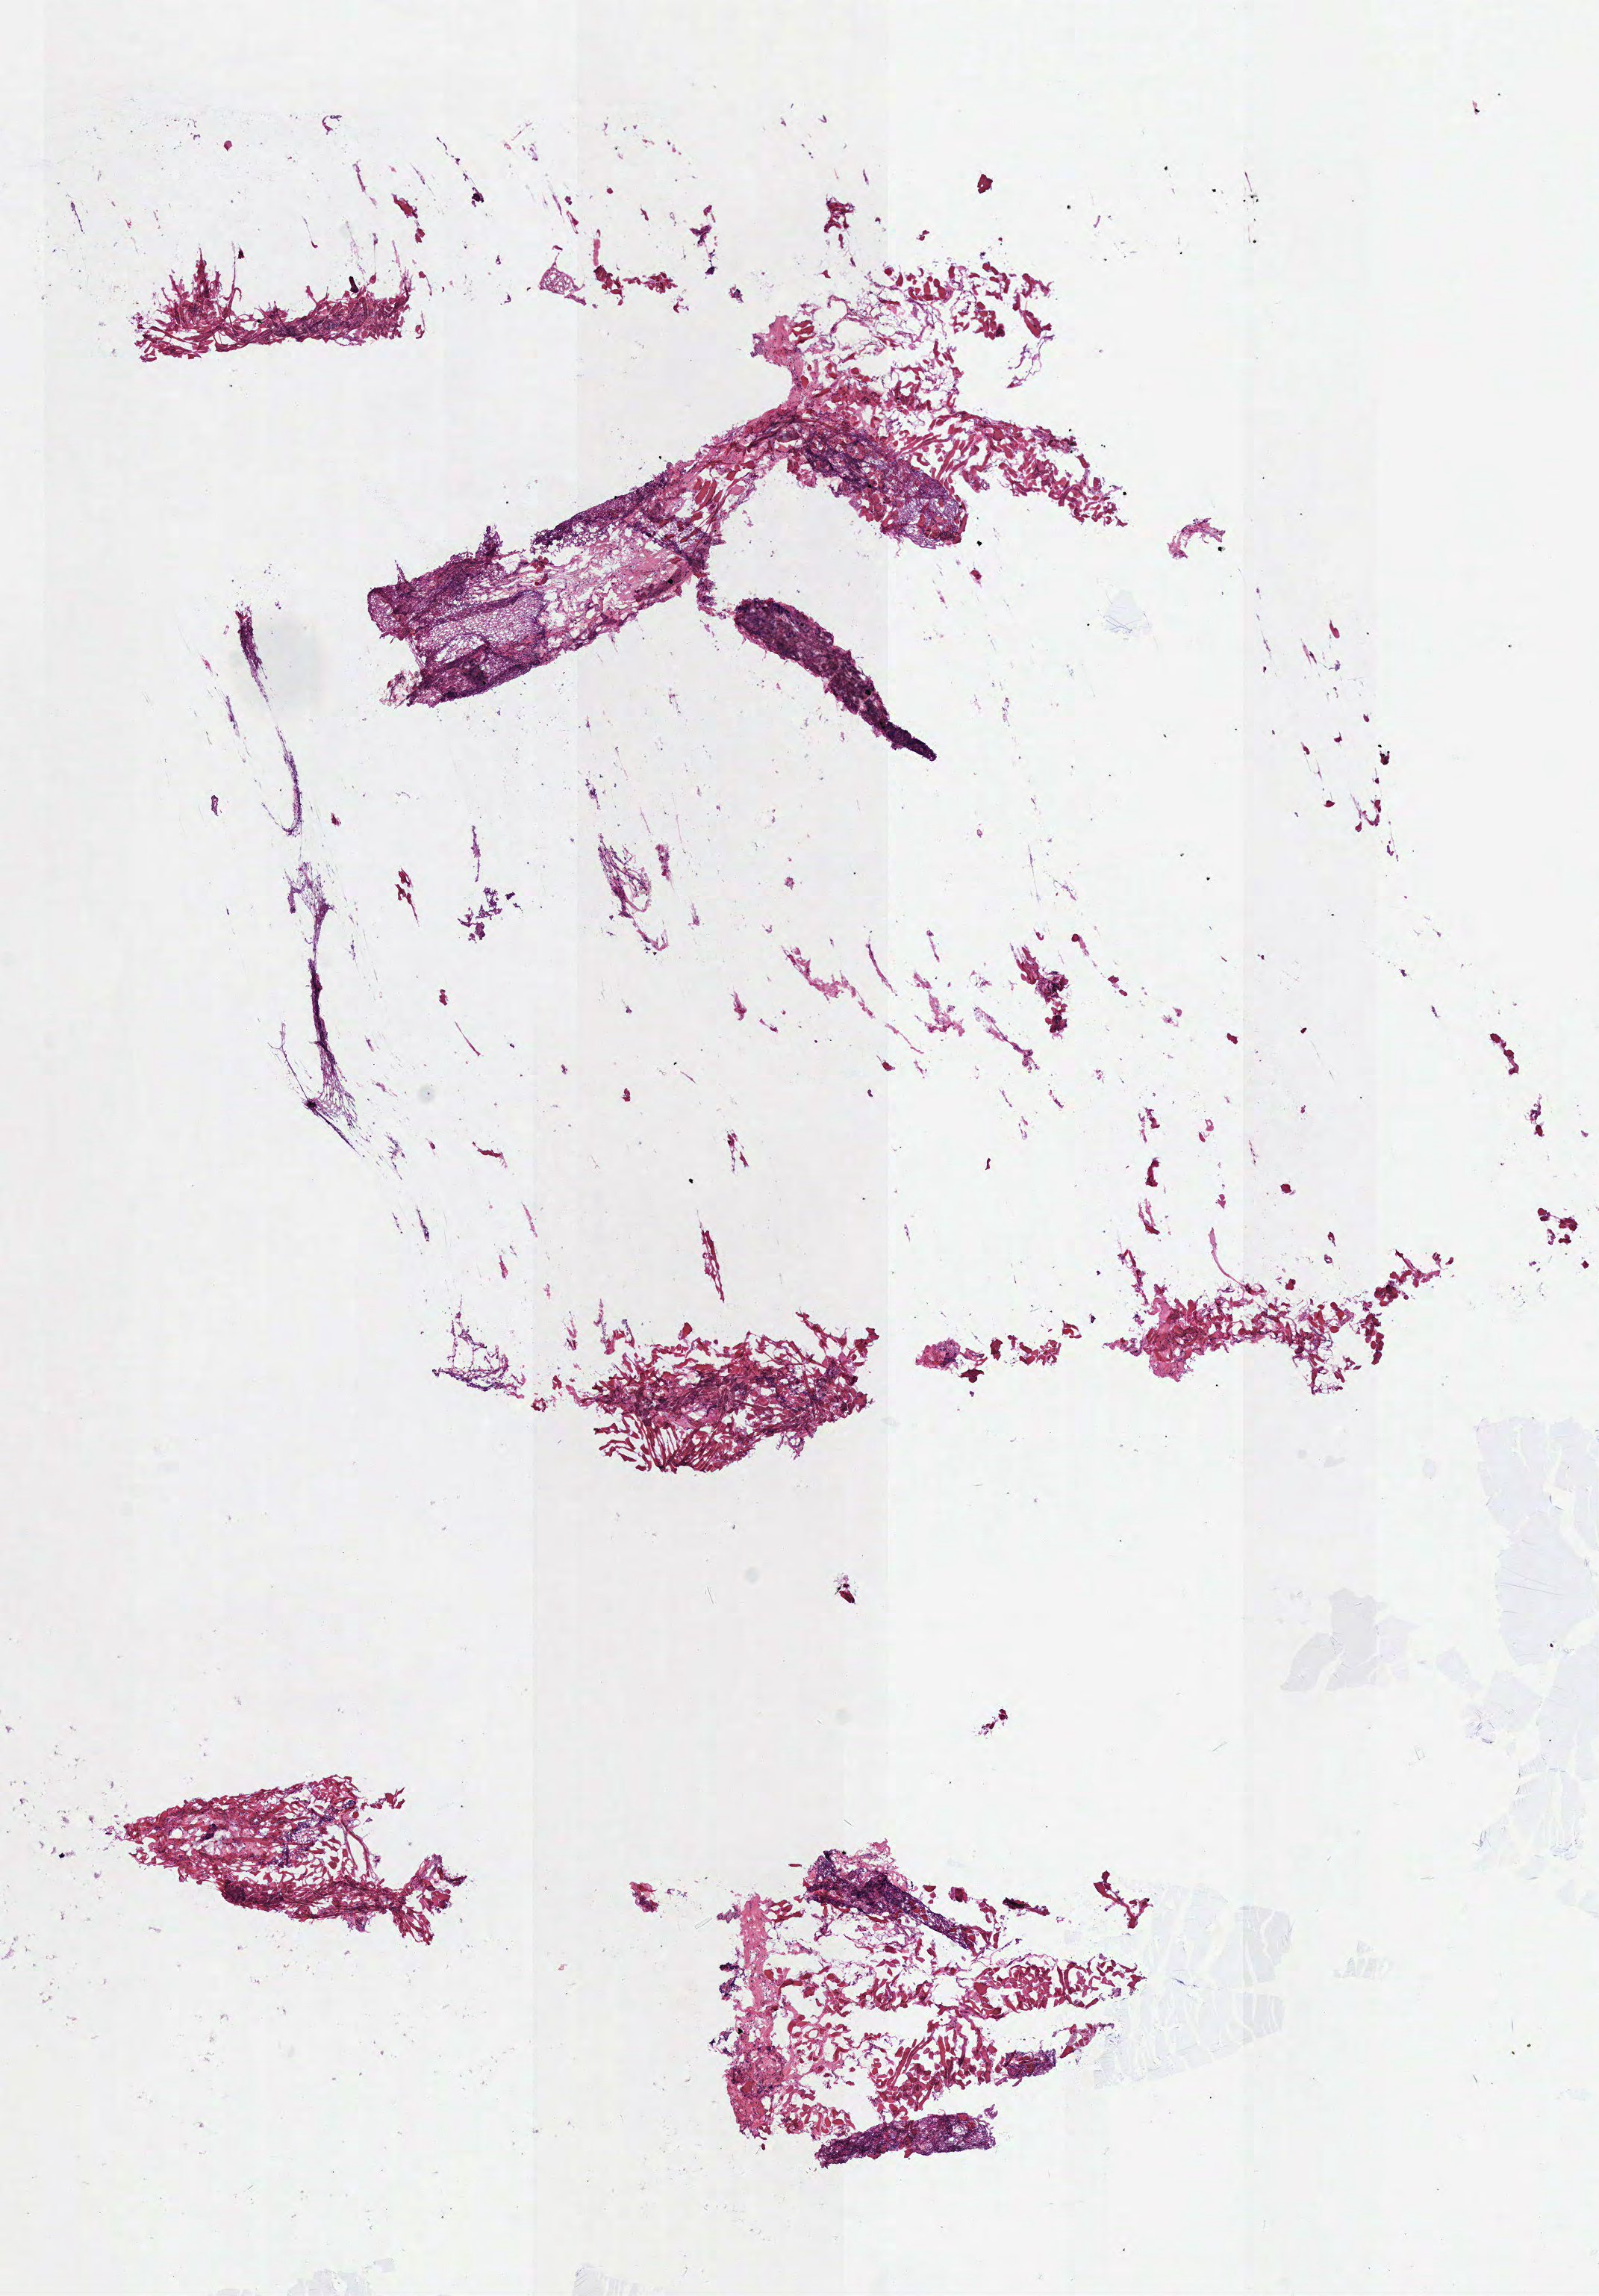
Whole-slide histology image, Hematoxylin and eosin (H&E) stained, a low-resolution overview of the entire scanned area, about 8.4 x 12.1 mm (from a 40x scan). Frozen section from the top of the tissue portion. Head and neck, solid tissue normal (non-tumour tissue) sample. Patient: male, age at initial diagnosis 67 years.
This section: solid tissue normal sample (biorepository sample class). Patient diagnosis: Squamous cell carcinoma, NOS (tongue, NOS).